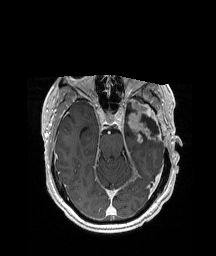
Brain MRI from a brain-tumour surgery series, one axial slice; slice 130 of 208 in the series (ordered by position); T1-weighted post-contrast; 1 mm slice thickness; 216 × 256 image matrix. Case-level facts recorded for this patient, not image findings: histopathology: Glioblastoma; WHO grade: 4; IDH mutation: no; tumour location: Left Anterior/Superior Temporal.
Annotated regions visible in this slice (manually delineated by an expert):
- previous resection cavity: bounding box (x1, y1, x2, y2) in pixels: (140, 115, 159, 134)
- tumour: (123, 99, 158, 144)